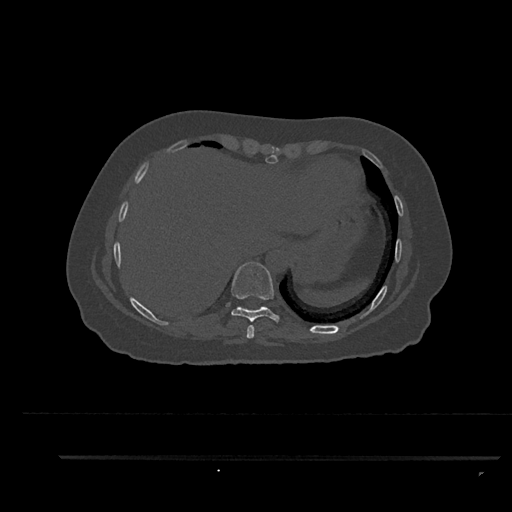
CT including the spine, one axial slice. Position 412 of 797 along the scan axis. Reconstruction kernel Br40s/3. 120 kVp. Bone window (W 1800 / L 400 HU). 0.5 mm slice thickness. 512 × 512 image matrix. Patient: female, 44 years. From the clinical record (not read from this slice): primary cancer: renal.
Structures marked on this image (semi-automatically segmented with operator editing):
- T8 vertebra: box from (x=246, y=325) to (x=255, y=339) px
- T9 vertebra: (x=231, y=262)–(x=281, y=323)